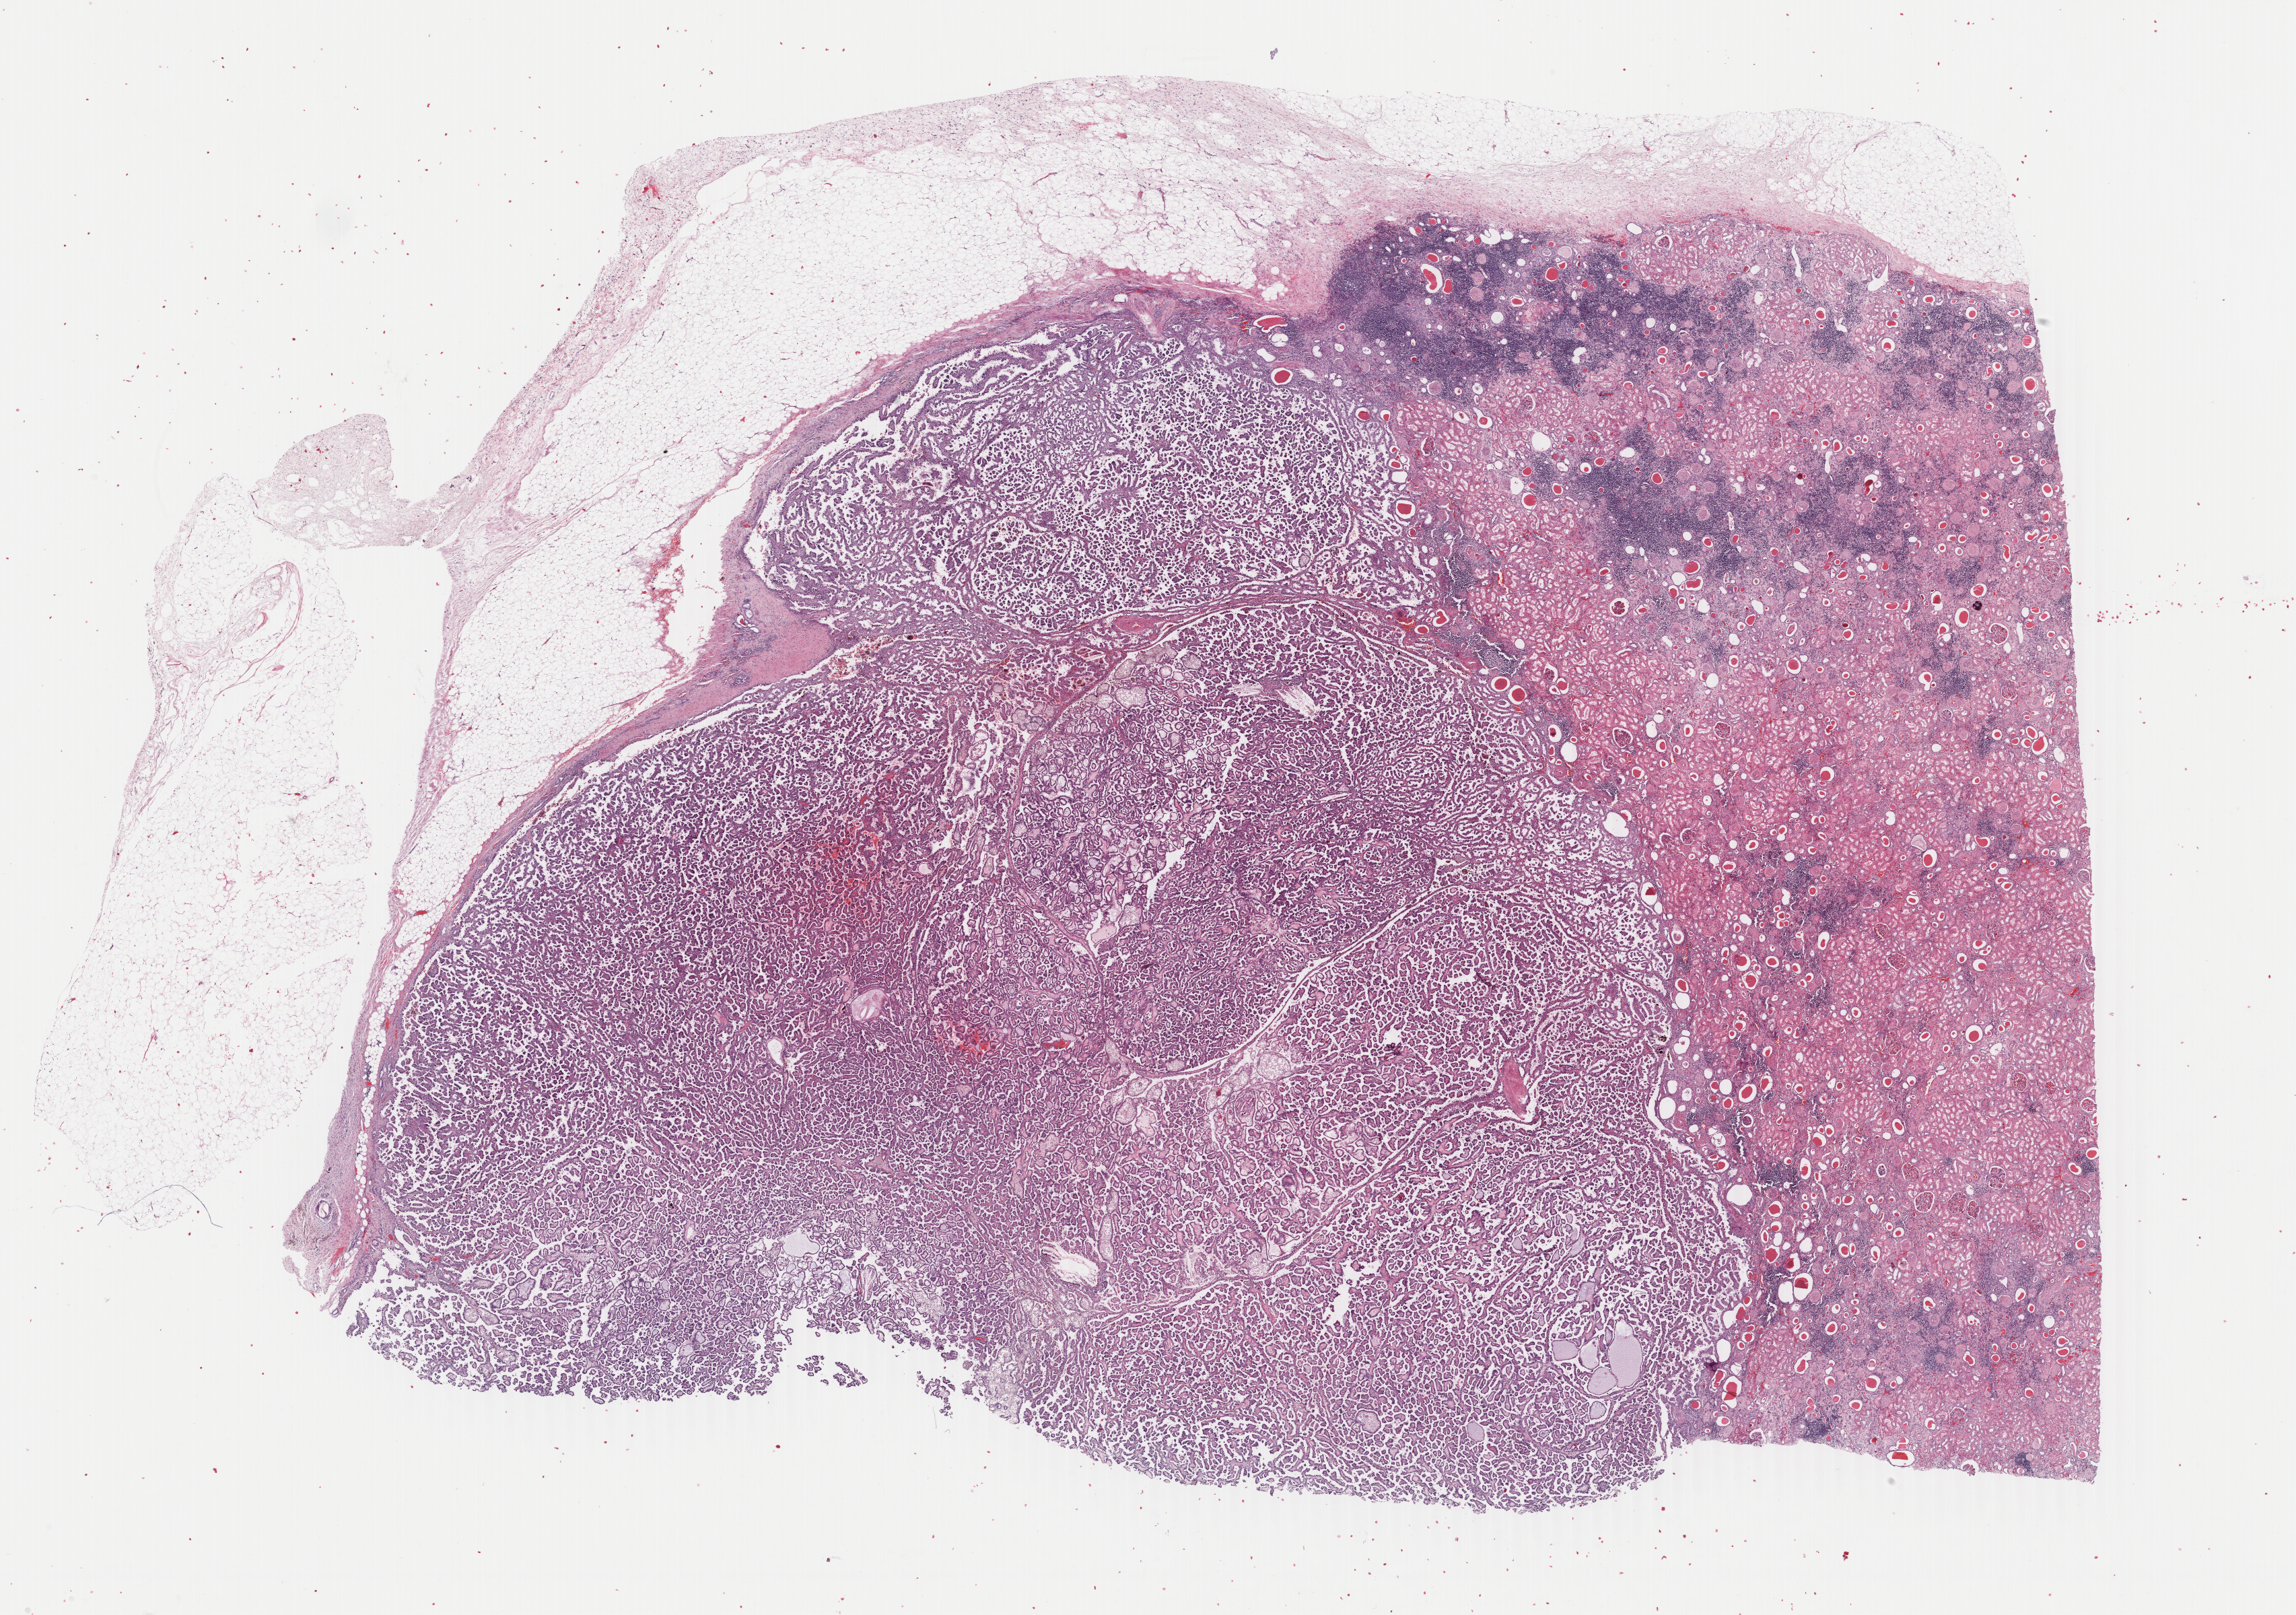
H&E-stained whole-slide image, low-resolution overview of the scanned area, about 27.1 x 19.1 mm; formalin-fixed paraffin-embedded (FFPE) diagnostic section; kidney, primary tumour sample. Male patient; age at initial diagnosis 77 years.
AJCC pathologic stage: I (7th edition). Histologic diagnosis: Papillary adenocarcinoma, NOS.